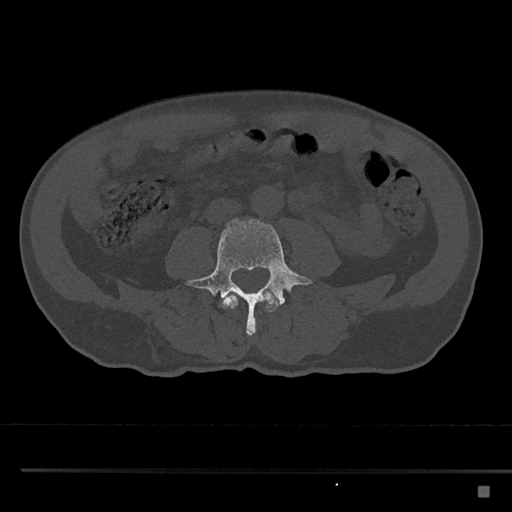
CT including the spine, one axial slice. Position 646 of 797 along the scan axis. Bone window (W 1800 / L 400 HU). 0.5 mm slice thickness. 512 × 512 image matrix, field of view 391 × 391 mm. Male patient, age 59 years. From the clinical record (not read from this slice): primary cancer: prostate.
Annotated regions visible in this slice (semi-automatic segmentation, software-assisted and operator-edited):
- L3 vertebra: bounding box [x1, y1, x2, y2] px = [222, 290, 278, 320]
- L4 vertebra: [186, 219, 312, 338]